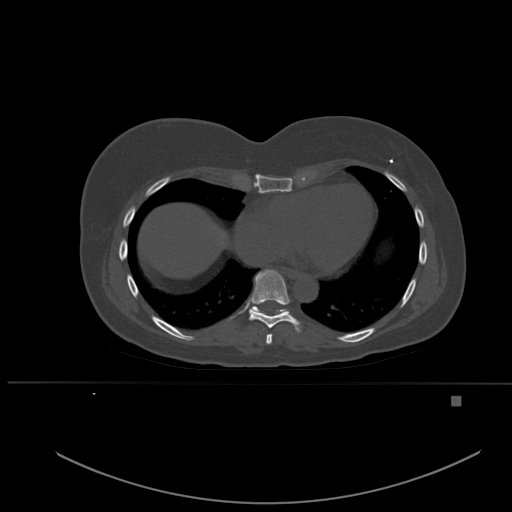
CT including the spine, one axial slice. Bone window (W 1800 / L 400 HU). 1.5 mm slice thickness. 512 × 512 image matrix. Female patient, age 49 years. From the clinical record (not read from this slice): primary cancer: breast; vertebrae with lytic lesions (as recorded): L3, T12, L4.
Outlined on this slice (semi-automatically segmented with operator editing):
- T7 vertebra: bounding box <266,334,273,344> (left, top, right, bottom; pixels)
- T8 vertebra: <248,269,301,332>
- T9 vertebra: <251,306,287,313>